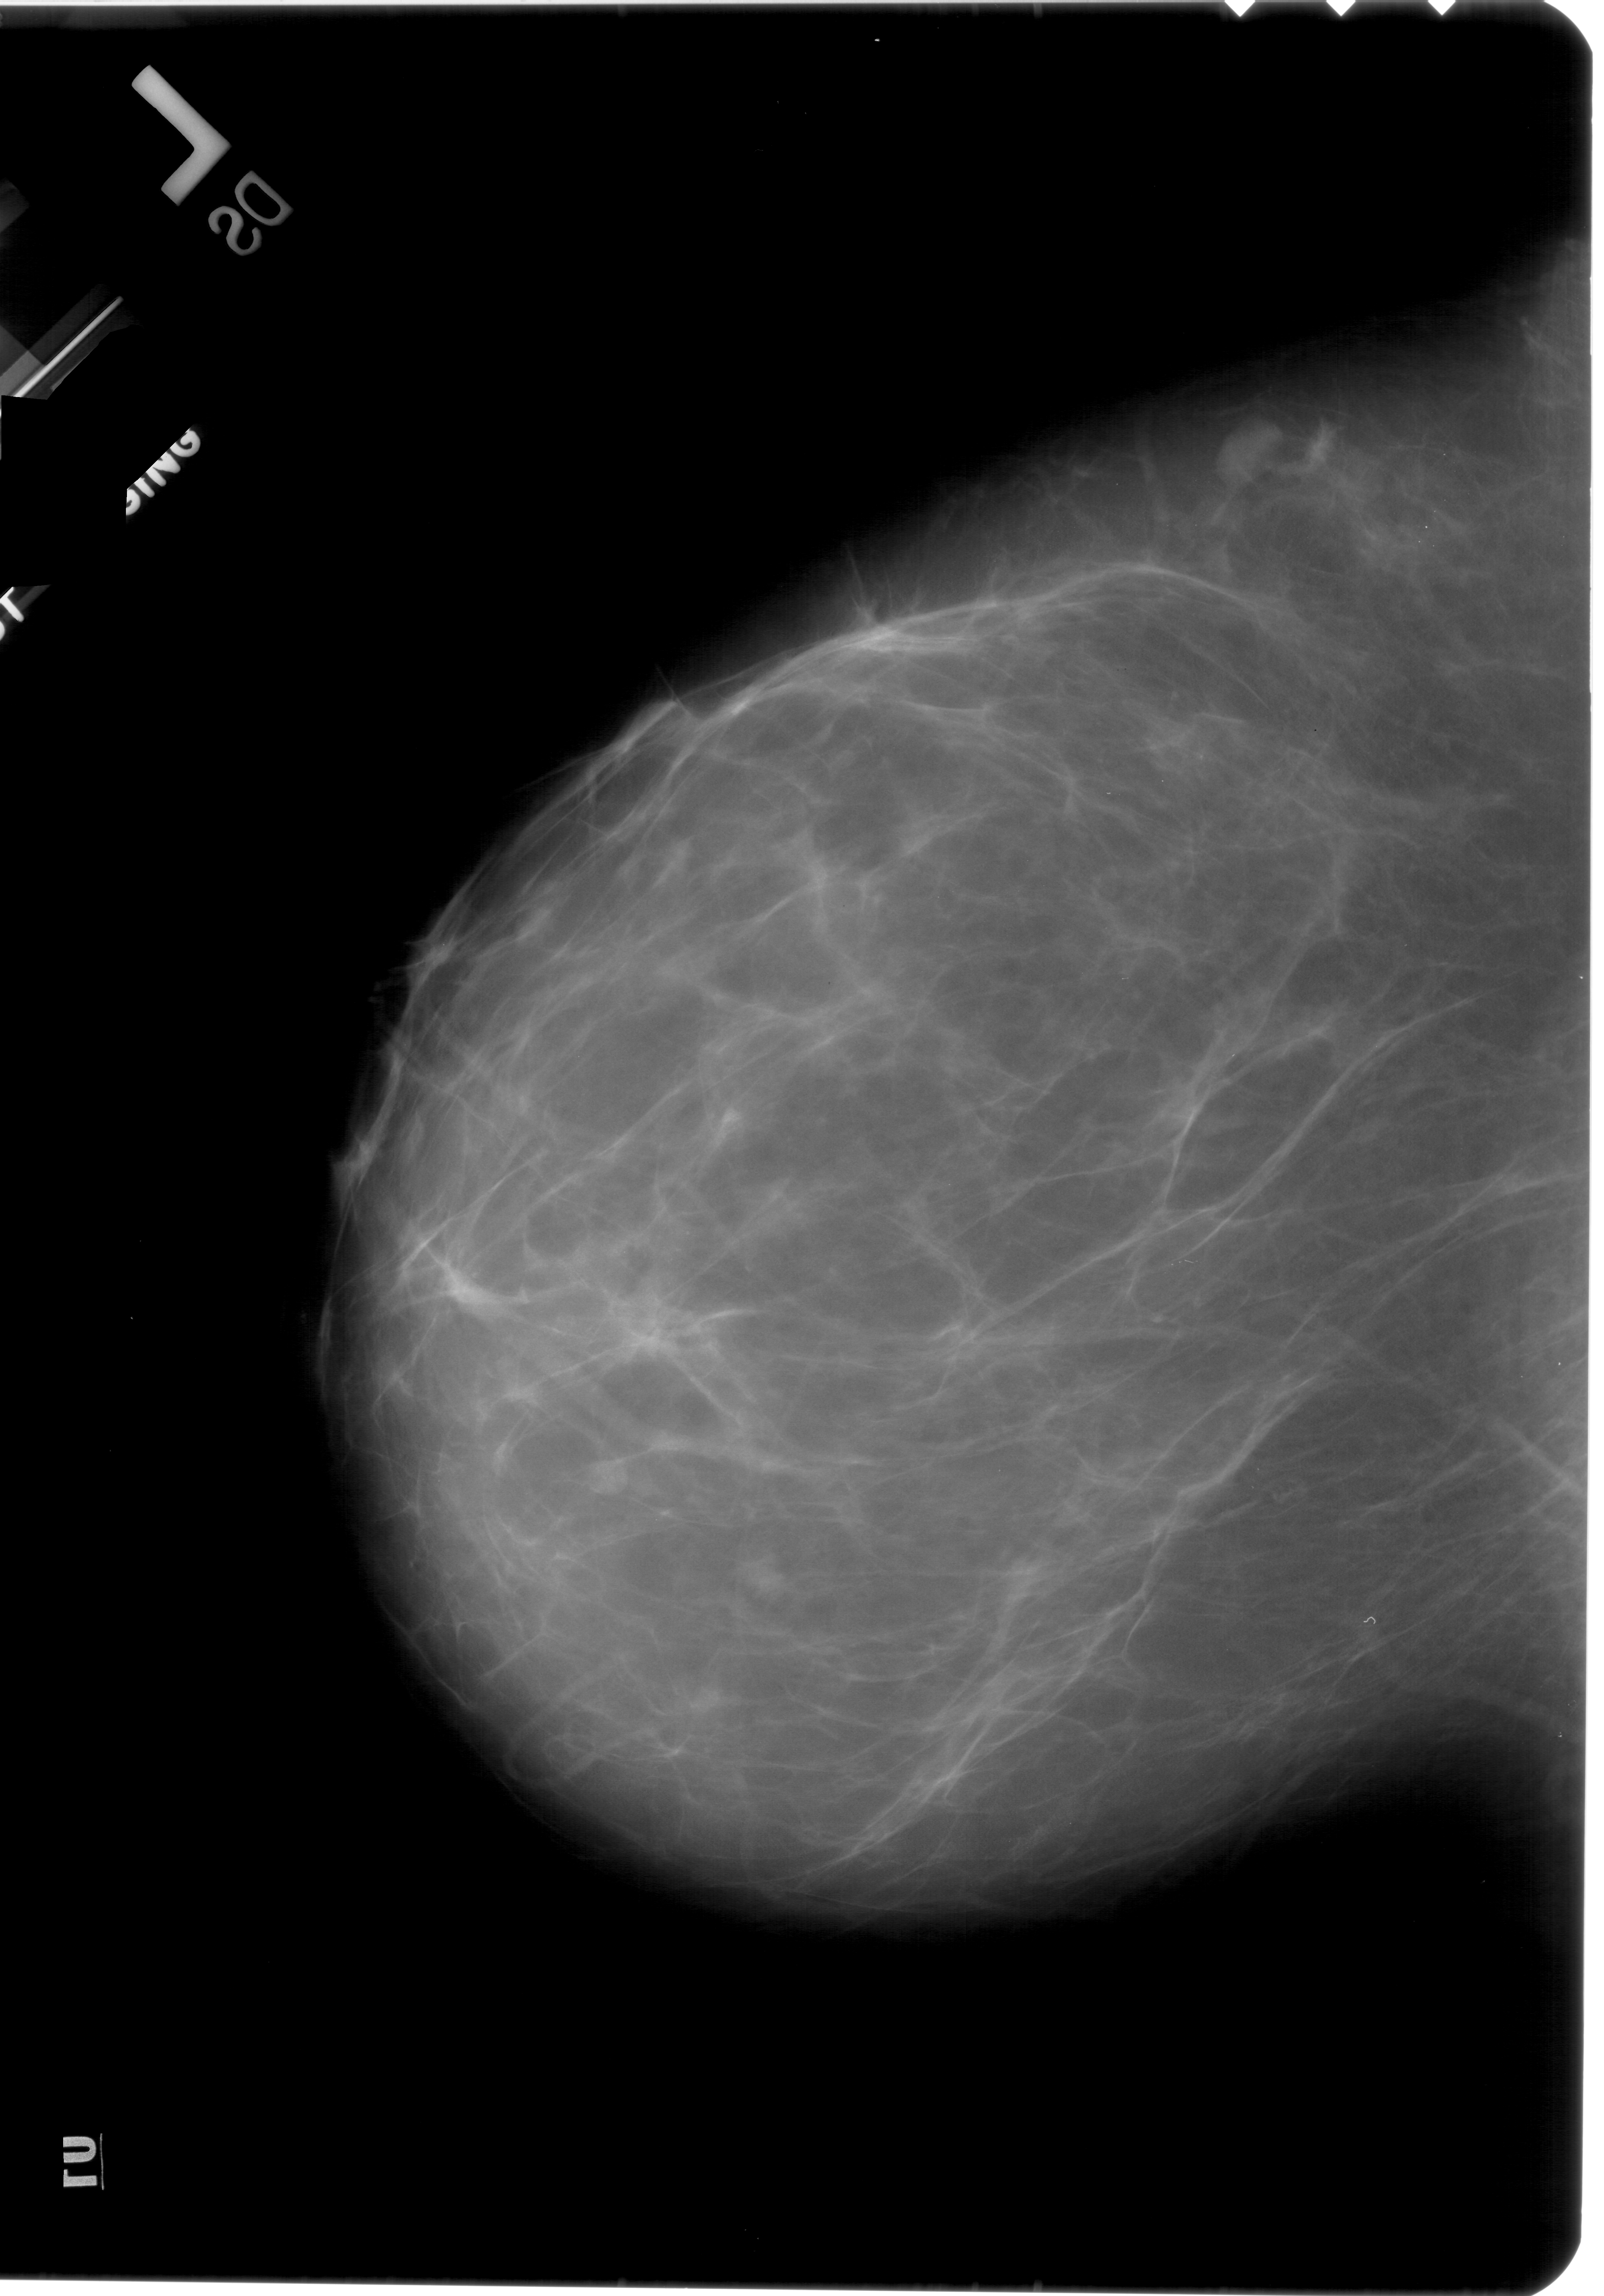
Mammogram (digitized film); left breast; craniocaudal (CC) view; 1604 × 2296 image matrix.
Expert-marked regions of interest on this image (one box per marked abnormality):
- calcifications, morphology pleomorphic, distribution clustered; BI-RADS assessment category 4; subtlety rating 1 on a 1 (subtle) to 5 (obvious) scale; pathology result (as recorded, not read from the image): benign: bounding box [x1, y1, x2, y2] px = [637, 1193, 715, 1292]